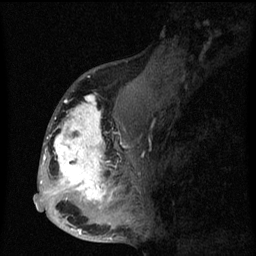
Breast MRI (dynamic contrast-enhanced), one sagittal slice; position 31 of 60 along the scan axis; dynamic contrast-enhanced series, image 2 of 3 at this slice position (ordered by acquisition); 1.5 T; TE 4.2 ms, TR 8 ms; 2 mm slice thickness; 256 × 256 image matrix, field of view 190 × 190 mm. Patient: female, 50 years.
Annotated regions visible in this slice (semi-automatically segmented with operator editing):
- analysis volume of interest (the breast-tissue region the enhancement analysis was run in; not a lesion): box from (x=43, y=90) to (x=142, y=216) px
- tumour enhancement mask (voxels above the 70 % enhancement threshold inside the analysis volume of interest): (x=43, y=95)–(x=128, y=210)